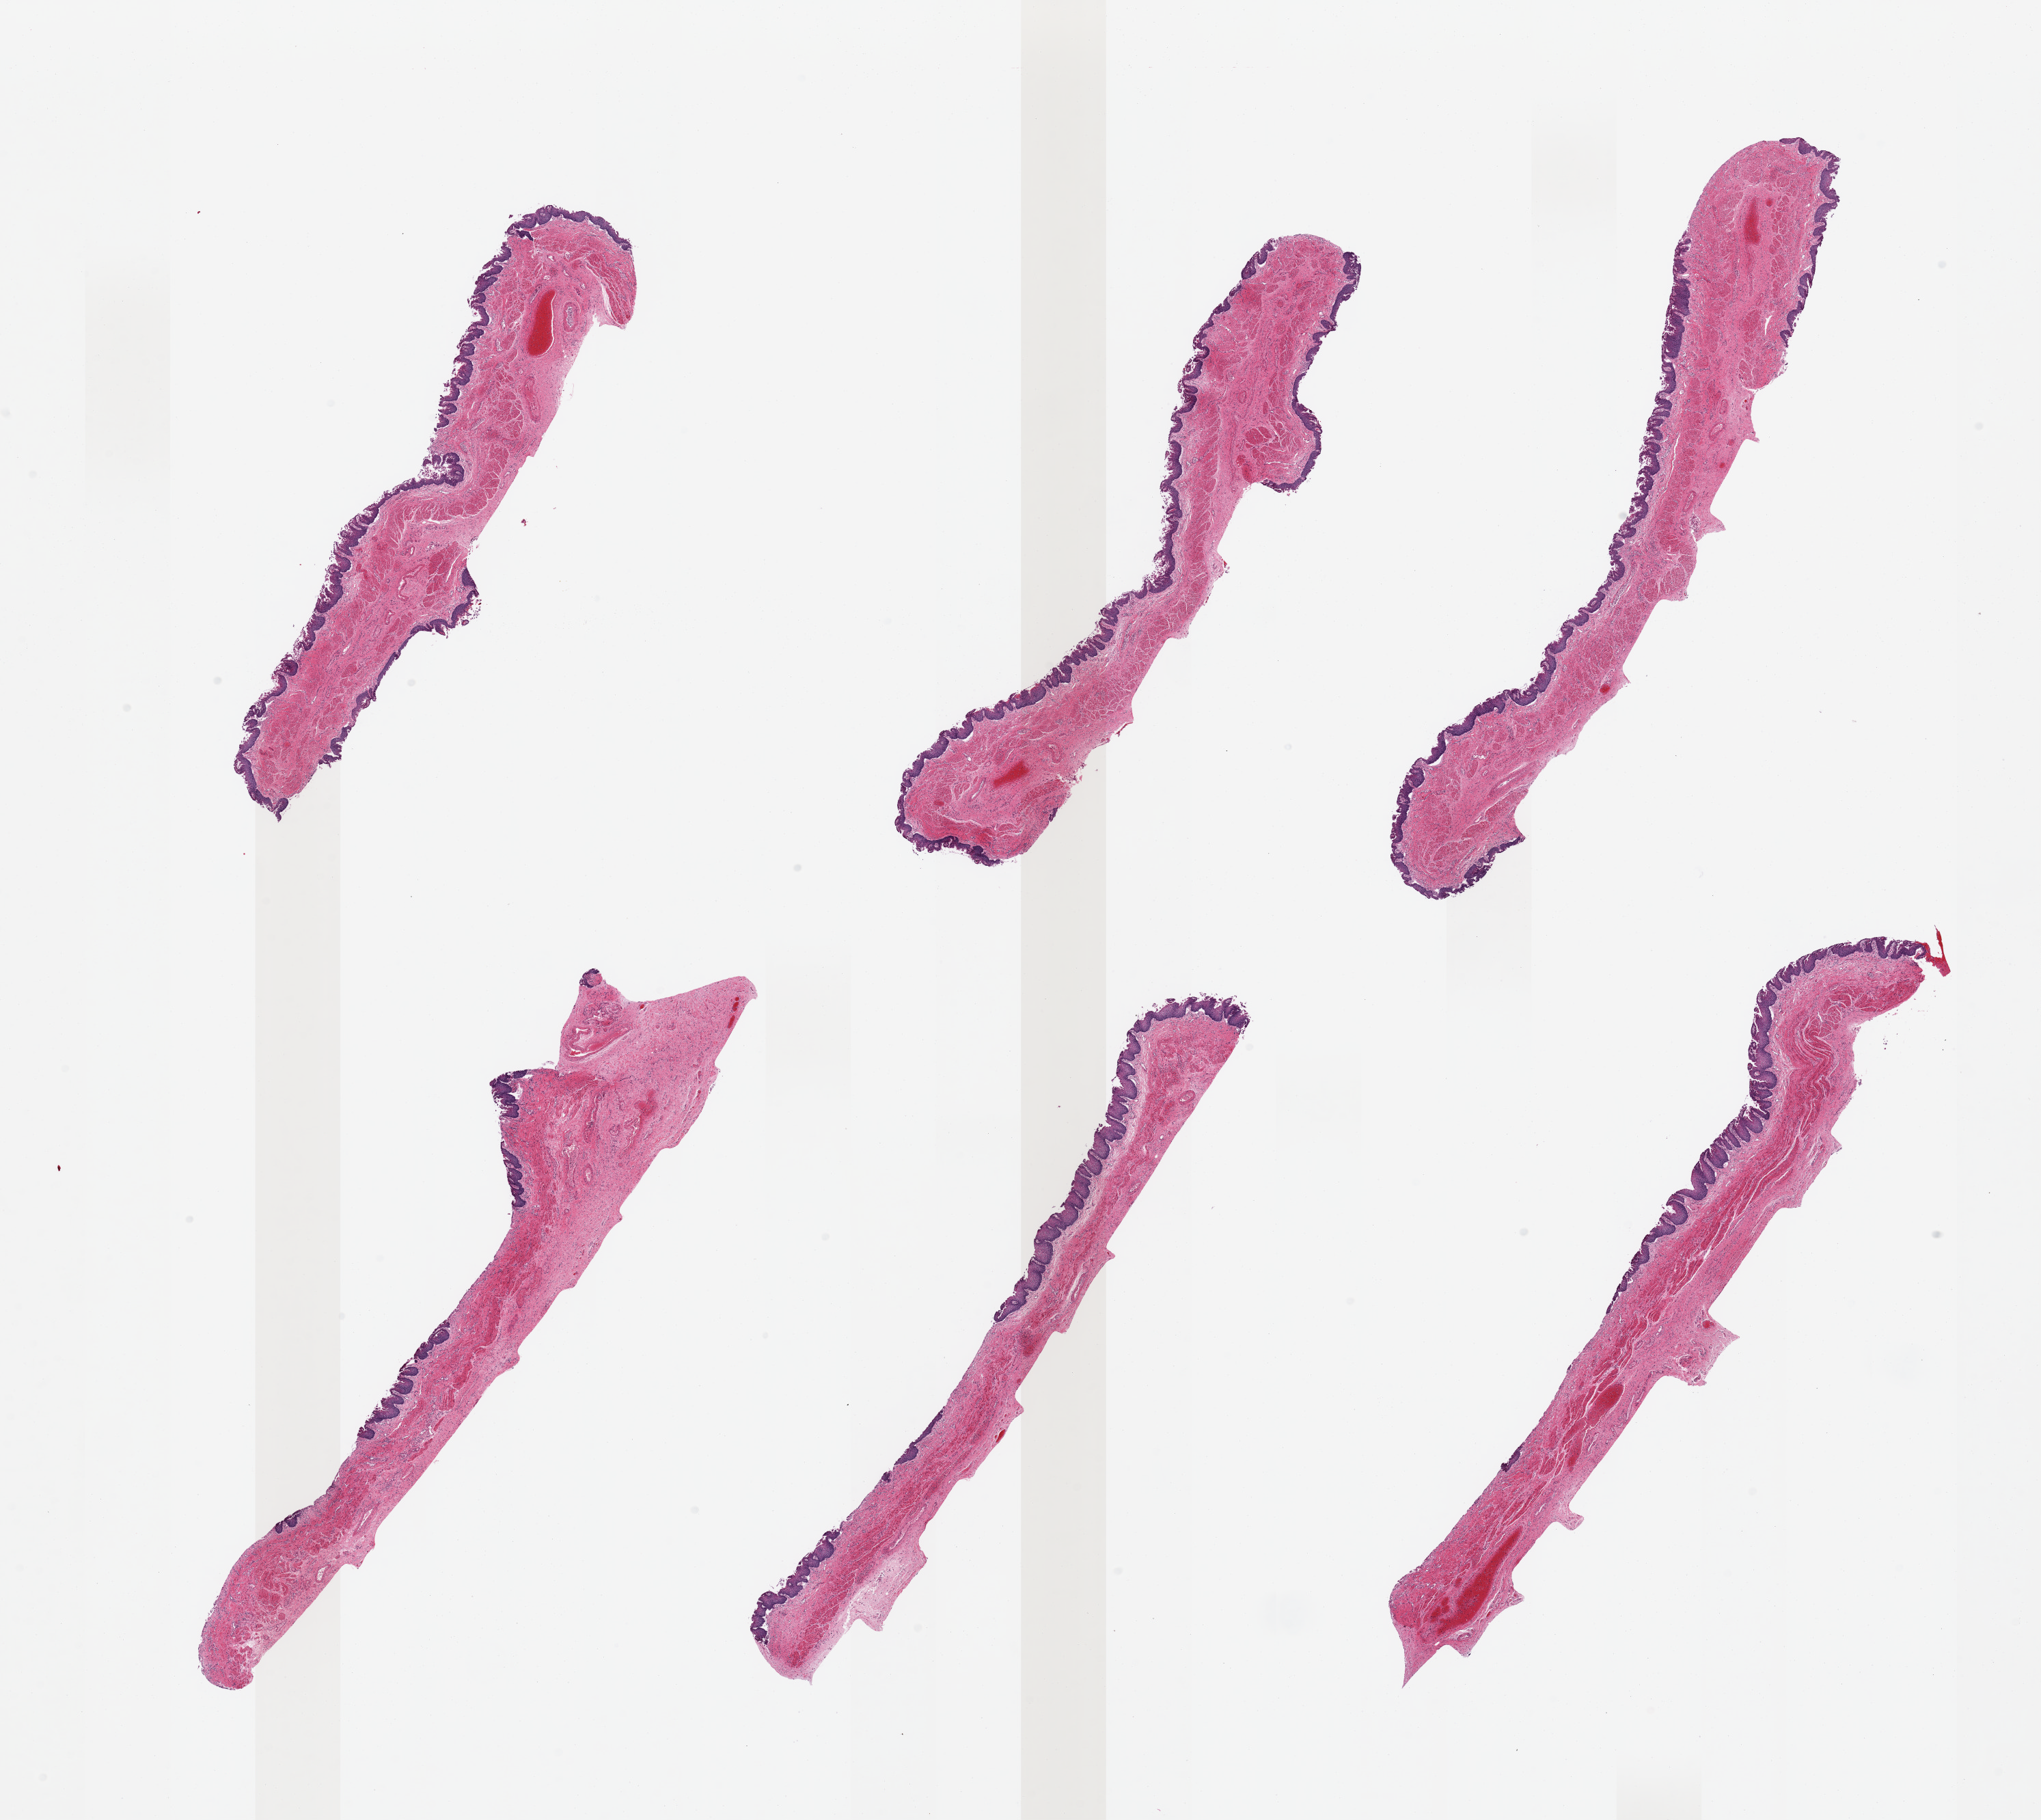
Hematoxylin and eosin (H&E) whole-slide image, brightfield, shown as a low-resolution overview of the whole scanned area (about 23.6 x 21.1 mm, slide scanned at 20x); PAXgene-fixed, paraffin-embedded tissue; section of esophageal mucous membrane (target tissue); tissue donor sample. Donor sex: female.
- pathologist's review note for this sample: 6 pieces, target squamous mucosa poorly preserved, sloughing, up to ~0.1mm, ~5-10% thickness